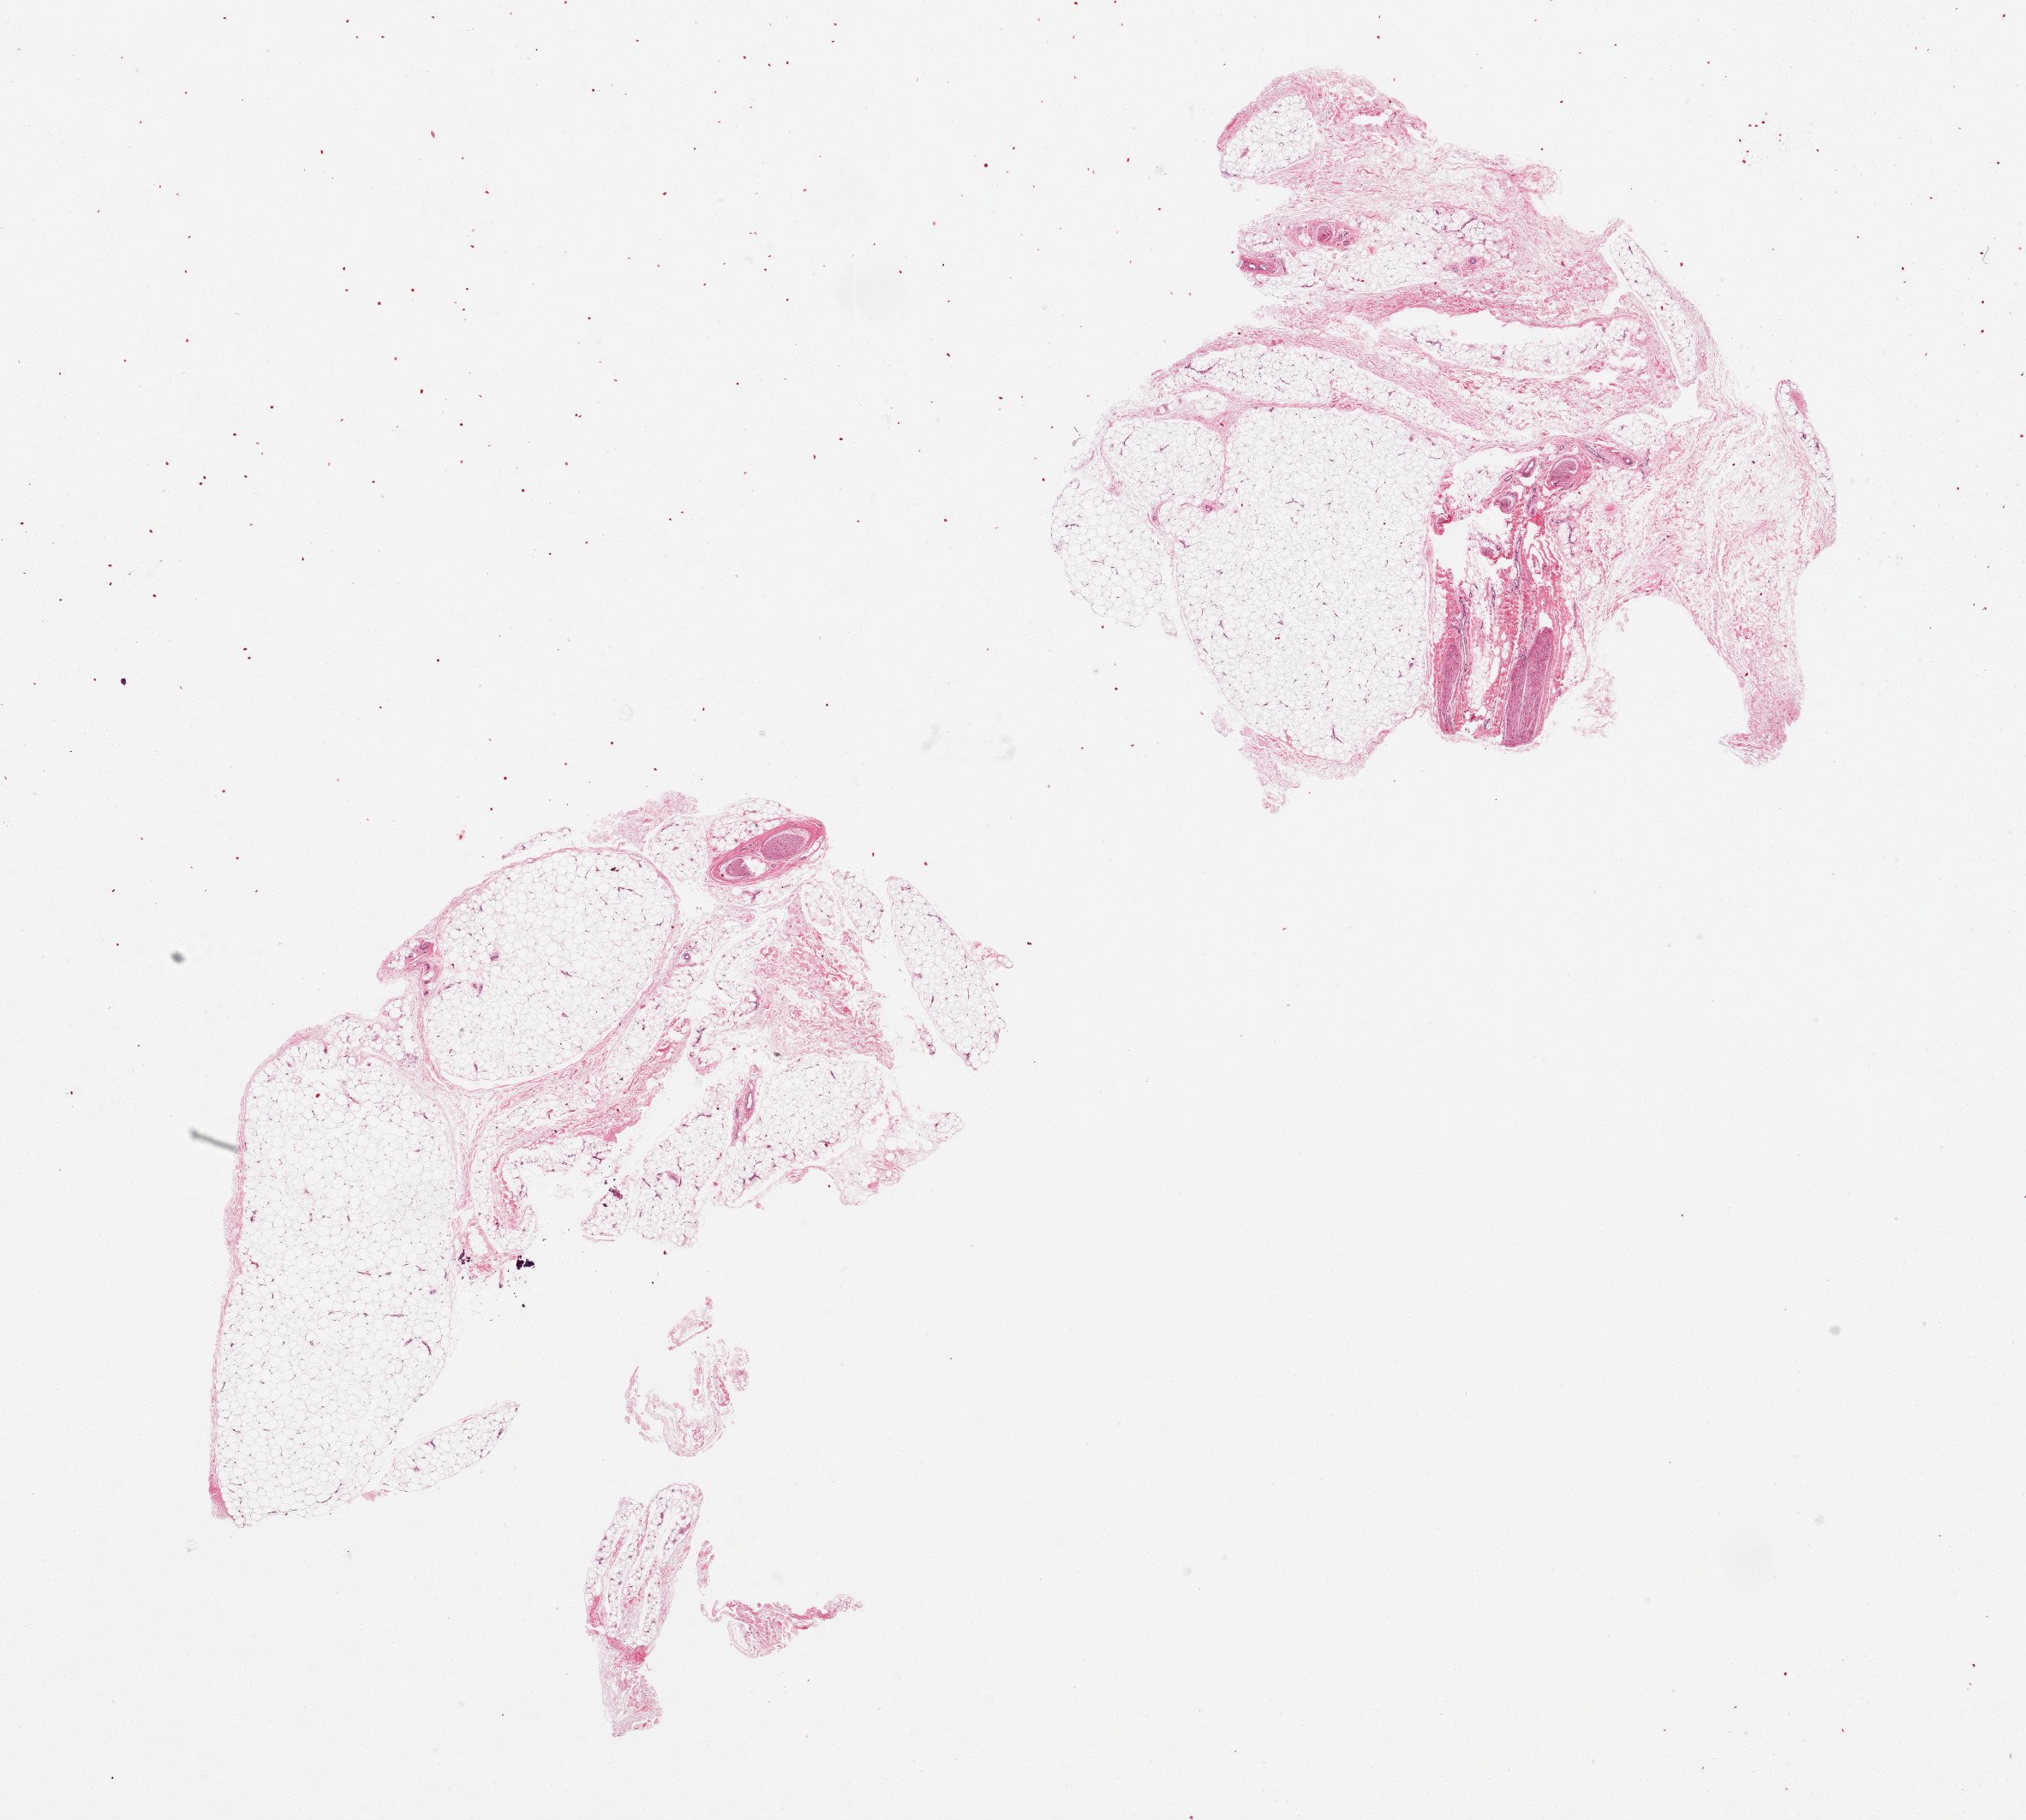
Whole-slide image, hematoxylin and eosin (H&E) stain — shown as a low-resolution overview of the whole scanned area (about 18.7 x 16.8 mm); PAXgene-fixed, paraffin-embedded tissue; section of adipose tissue (target tissue); donor tissue sample.
* pathologist's review note for this sample: 2 pieces, 9x4 & 8x5 mm